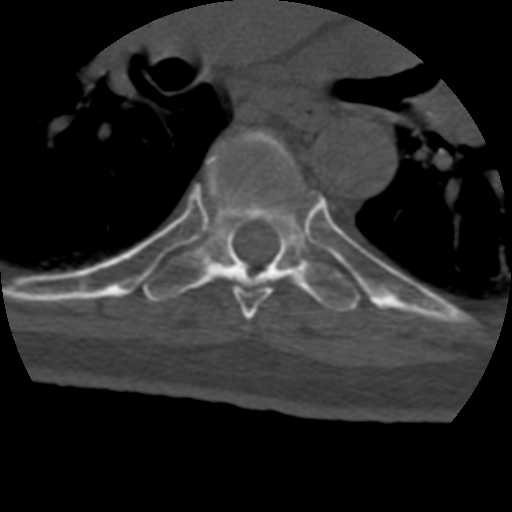
CT including the spine, one axial slice; position 290 of 399 along the scan axis; reconstruction kernel STANDARD; 120 kVp; bone window (W 1800 / L 400 HU); 1.25 mm slice thickness; 512 × 512 image matrix, field of view 160 × 160 mm. Patient age 69 years. From the clinical record (not read from this slice): primary cancer: prostate.
Annotated regions visible in this slice (semi-automatically segmented with operator editing):
- T6 vertebra: bounding box <230,133,303,319> (left, top, right, bottom; pixels)
- T7 vertebra: <143,132,361,312>